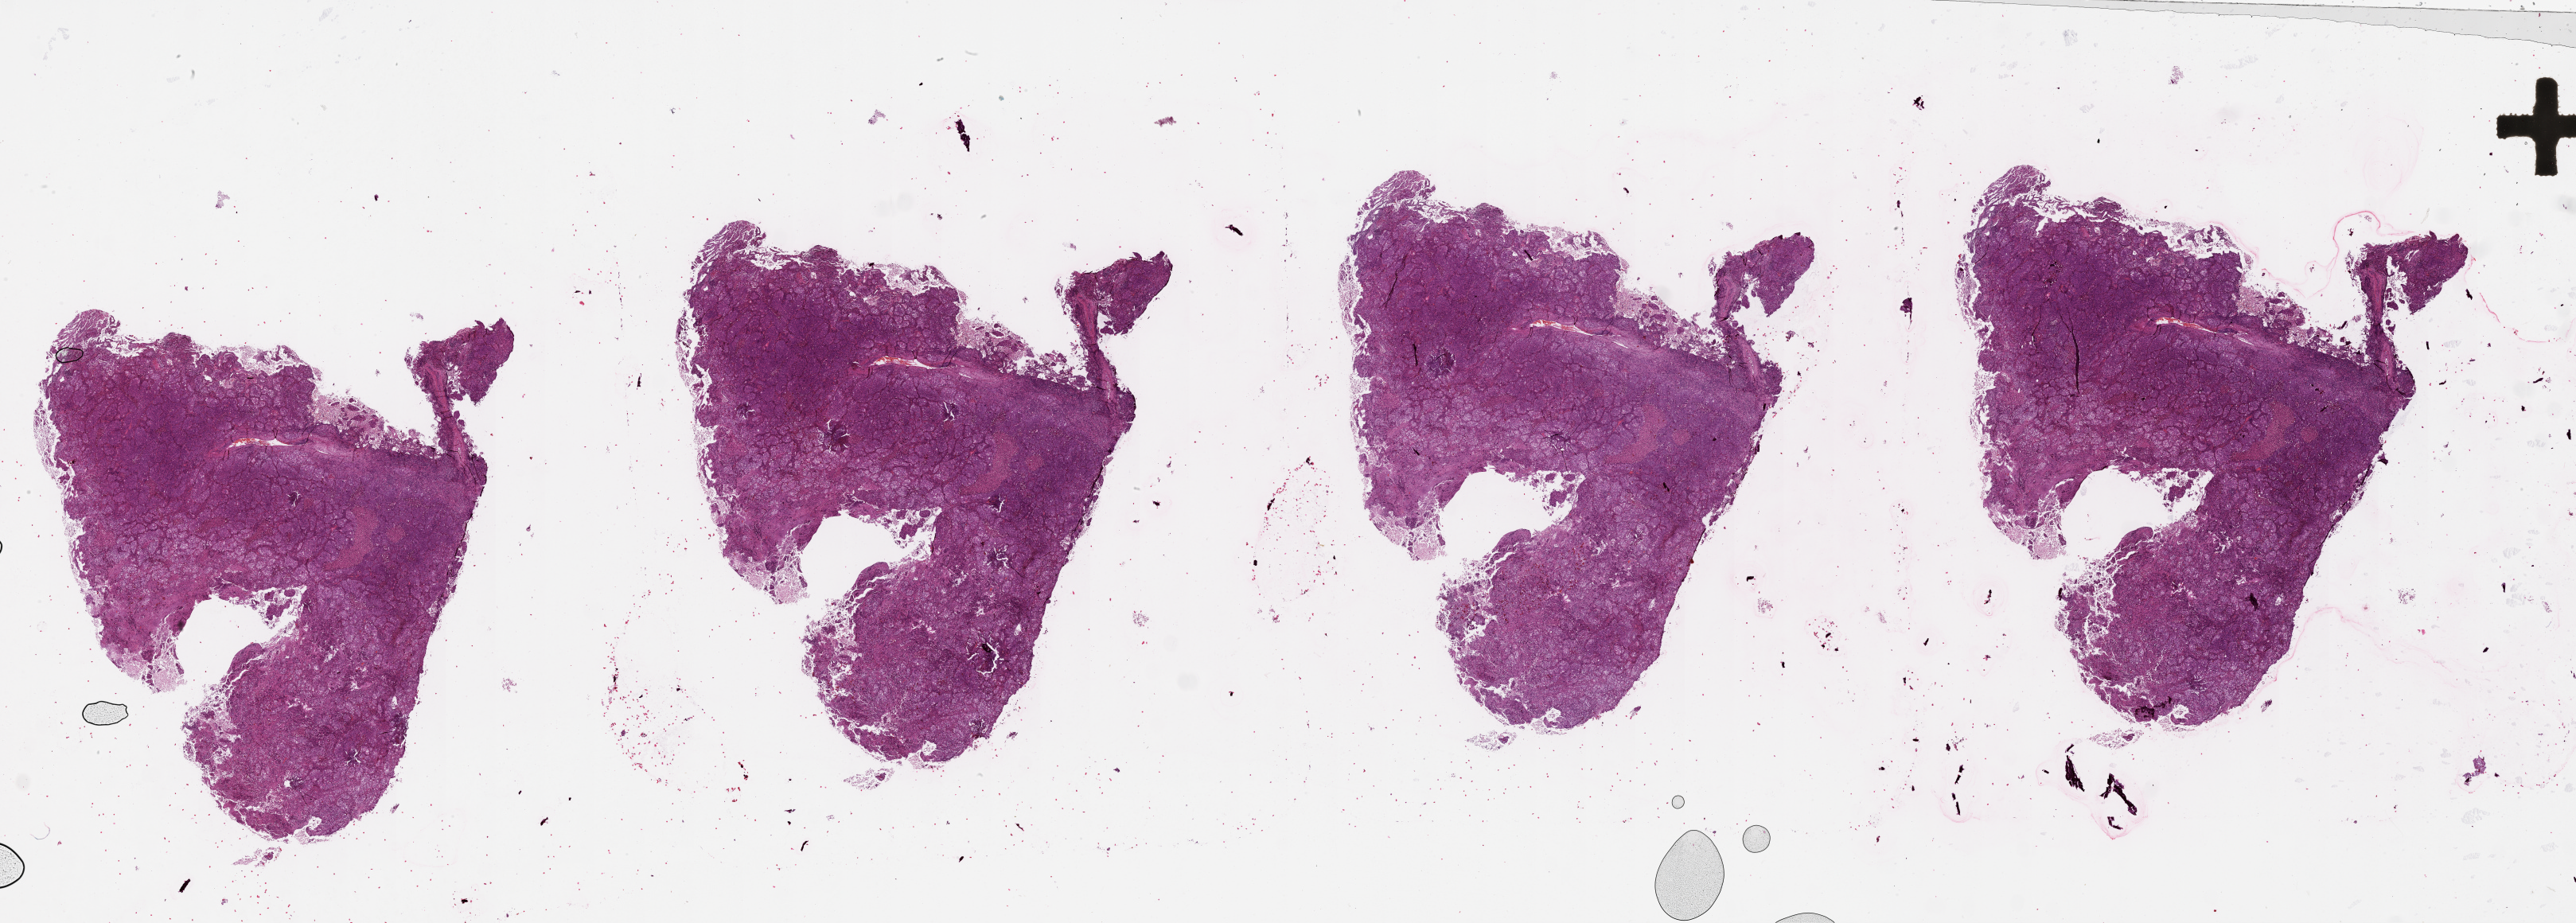
Digitized H&E tissue section (whole slide), a low-resolution overview of the entire scanned area, about 52.1 x 18.7 mm (acquisition: 20x scan). Lung, tissue type not recorded.
Patient diagnosis (cohort enrolment): lung adenocarcinoma (lung).